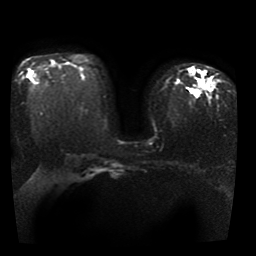
Breast MRI, one axial slice. Slice 25 of 41 in the series (ordered by position). Diffusion-weighted series; image 2 of 4 stored at this slice position (different b-values; order by instance number). 1.5 T. 5 mm slice thickness. 256 × 256 image matrix. Female patient.
Outlined on this slice (manually delineated by an expert):
- tumour on diffusion-weighted imaging: bounding box [x1, y1, x2, y2] px = [197, 72, 204, 87]